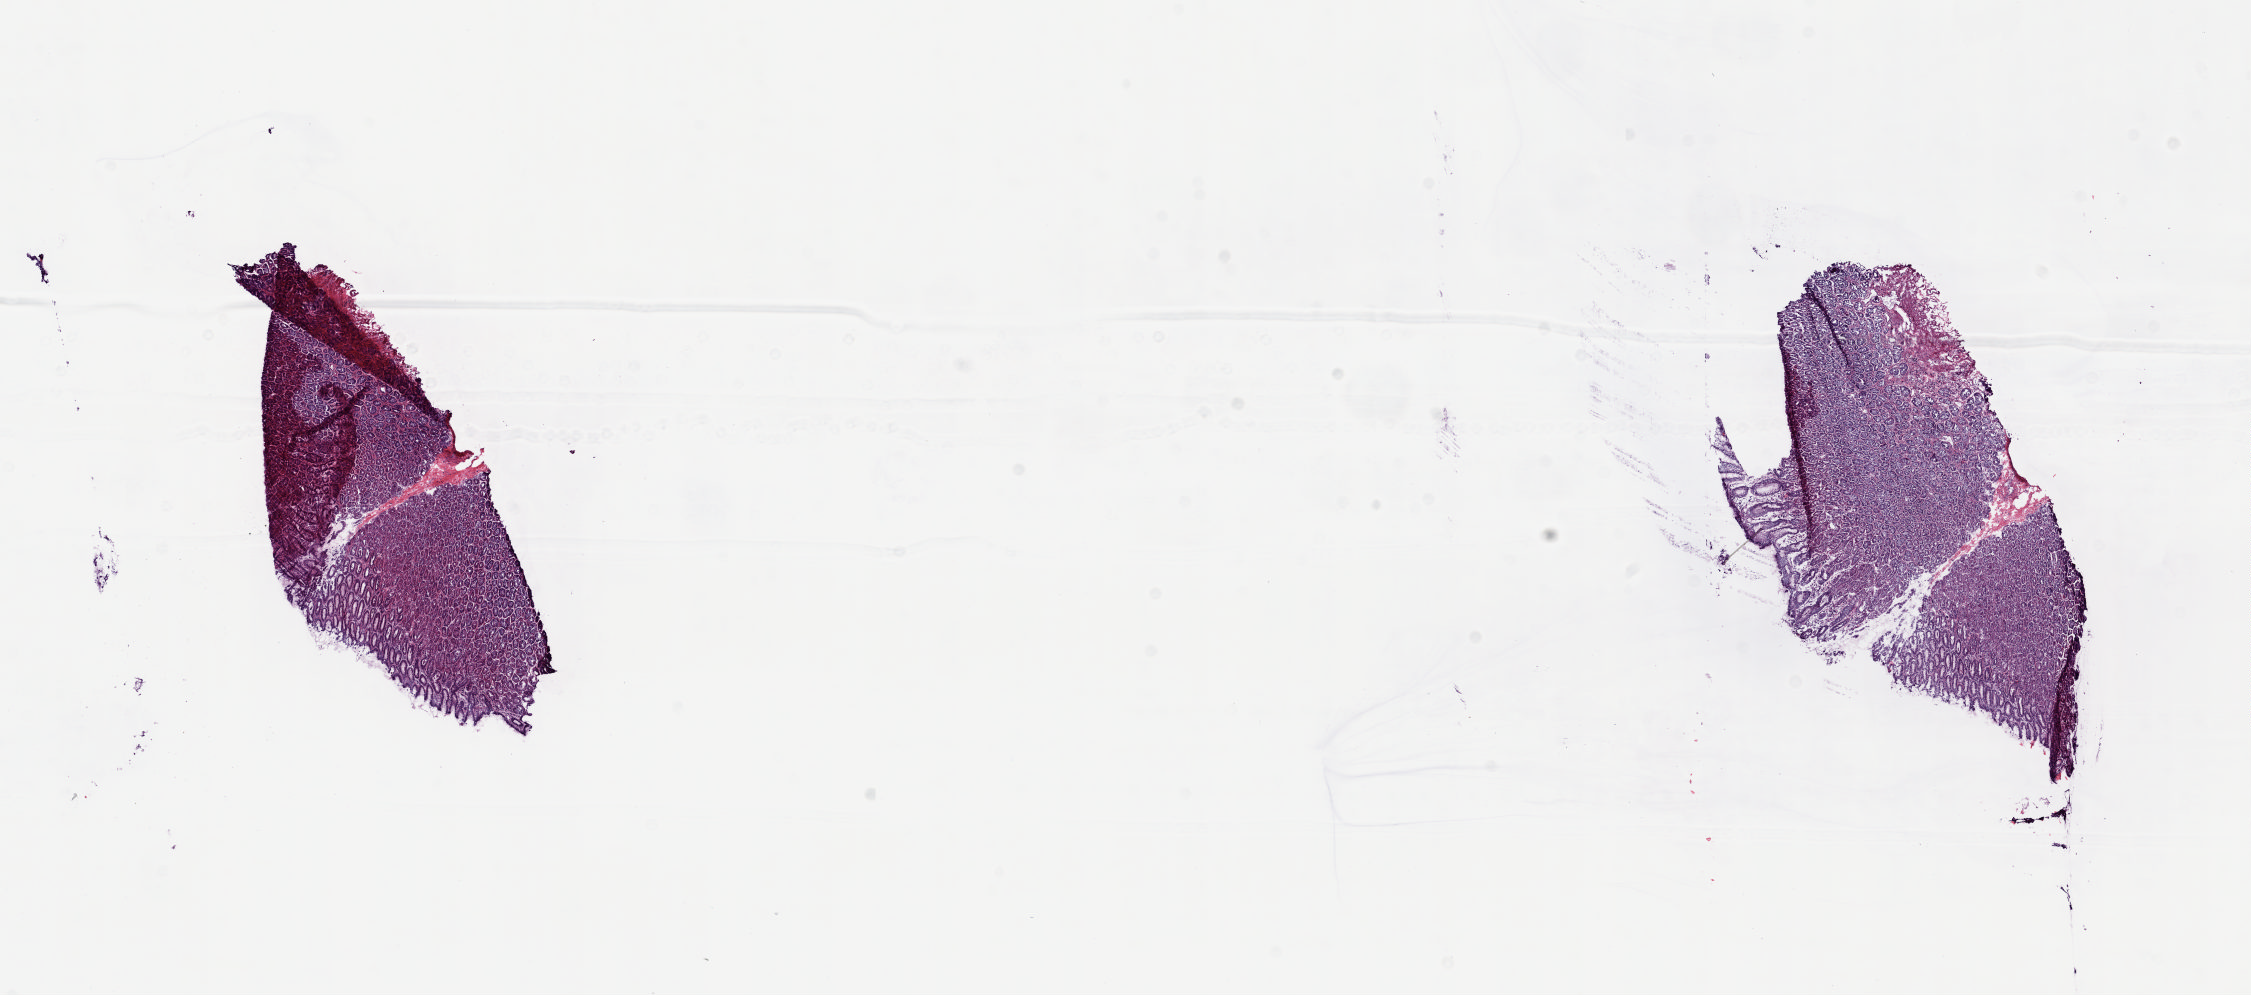
H&E whole-slide image — a low-resolution overview of the entire scanned area, about 17.9 x 7.9 mm (acquisition: 20x scan), frozen section from the top of the tissue portion, sample: solid tissue normal (non-tumour tissue), esophagus. Male patient; age at initial diagnosis 55 years. Pathologist review of this section (percent, as recorded): tumour cells 0%, tumour nuclei 0%, normal cells 100%, stromal cells 0%, necrosis 0%. Inflammatory infiltration, as recorded: lymphocyte infiltration 5%, monocyte infiltration 0%, neutrophil infiltration 0%.
This section: solid tissue normal (non-tumour) sample from the same patient. Patient diagnosis: Adenocarcinoma, NOS (lower third of esophagus).